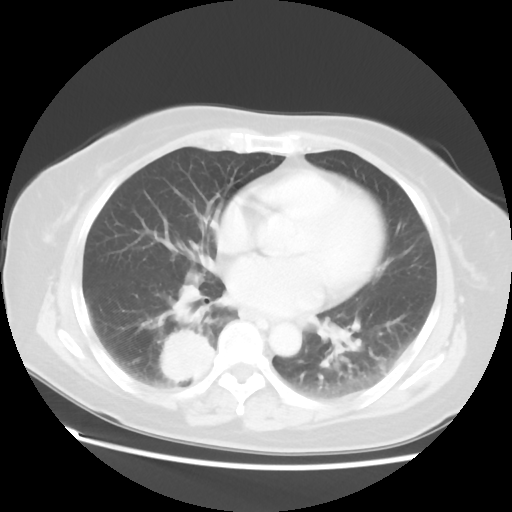
Chest CT, one axial slice. Slice 26 of 52 in the series (ordered by position). Reconstruction kernel STANDARD. Lung window (W 1500 / L -600 HU). 512 × 512 image matrix, field of view 356 × 356 mm. Female patient, age 69 years. From the clinical record (not read from this slice): clinical TNM (as recorded): T2 N1 M1a.
Structures marked on this image (rectangle marked by the reading radiologist):
- lung tumour (recorded histology: adenocarcinoma): box from (x=154, y=325) to (x=216, y=393) px